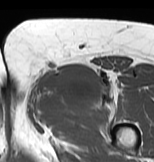
MRI of an extremity soft-tissue mass, one axial slice; slice 42 of 83 in the series (ordered by position); MR volume resampled by the dataset authors to the PET/CT grid (not the native acquisition matrix); 3.27 mm slice thickness; 154 × 162 image matrix. Female patient. From the clinical record (not read from this slice): histological type: myxofibrosarcoma; grade: intermediate; site of the primary tumour: left thigh.
Structures marked on this image (expert contour drawn on MRI and transferred to this co-registered scan by the dataset authors):
- gross tumour volume including surrounding oedema: bounding box [x1, y1, x2, y2] px = [26, 66, 121, 119]
- gross tumour volume (mass): [42, 66, 100, 104]